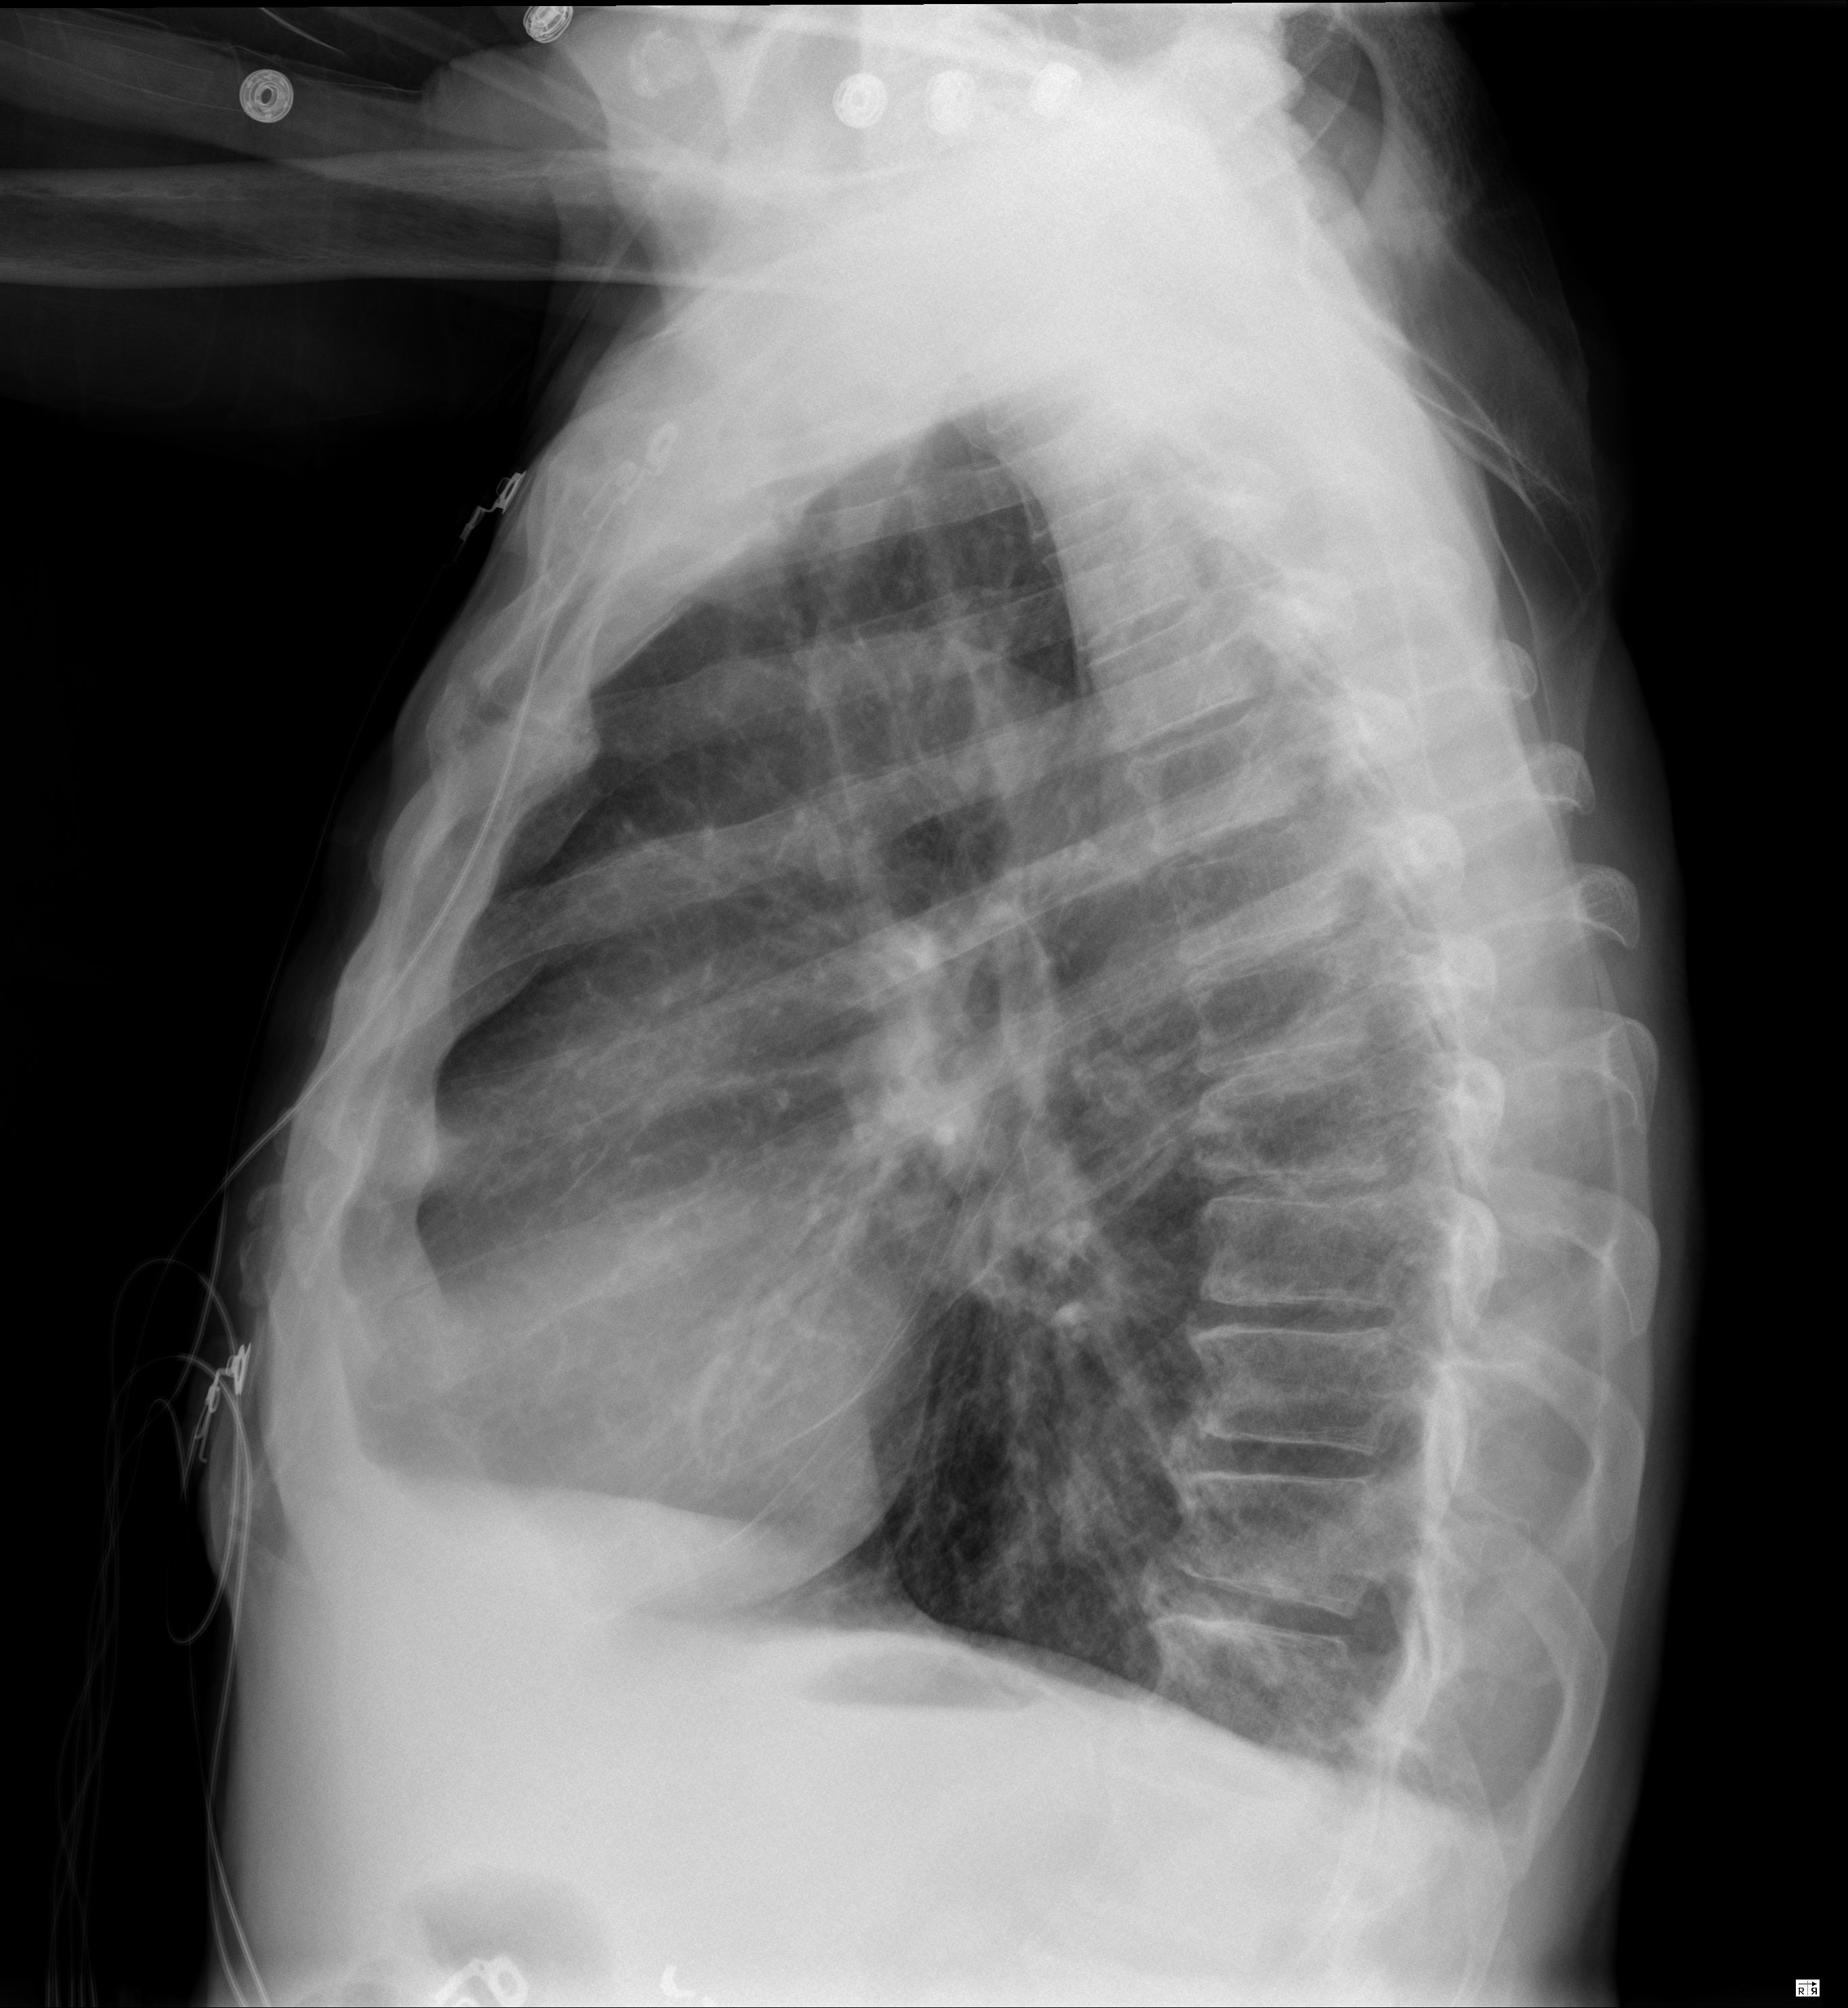
Chest radiograph, lateral projection. Male patient, age 67 years; imaged 7 days before the COVID-19 diagnosis.
Key findings recorded by the radiologist: Persistent trace left pleural effusion.